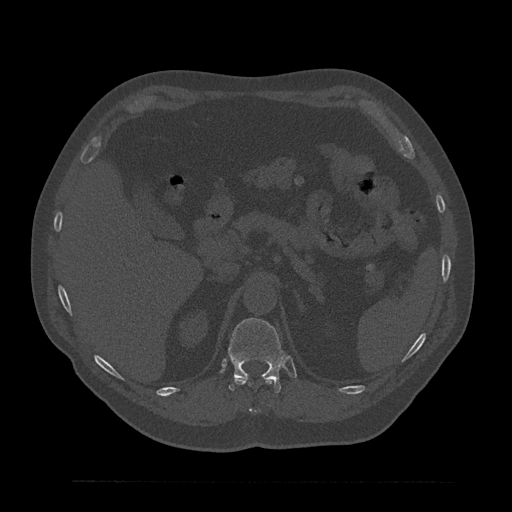
CT including the spine, one axial slice. Position 253 of 797 along the scan axis. Bone window (W 1800 / L 400 HU). 512 × 512 image matrix, field of view 430 × 430 mm. Male patient, age 61 years. Case-level facts recorded for this patient, not image findings: primary cancer: prostate.
Annotated regions visible in this slice (semi-automatically segmented with operator editing):
- T11 vertebra: bounding box [x1, y1, x2, y2] px = [234, 377, 274, 413]
- T12 vertebra: [228, 318, 285, 393]